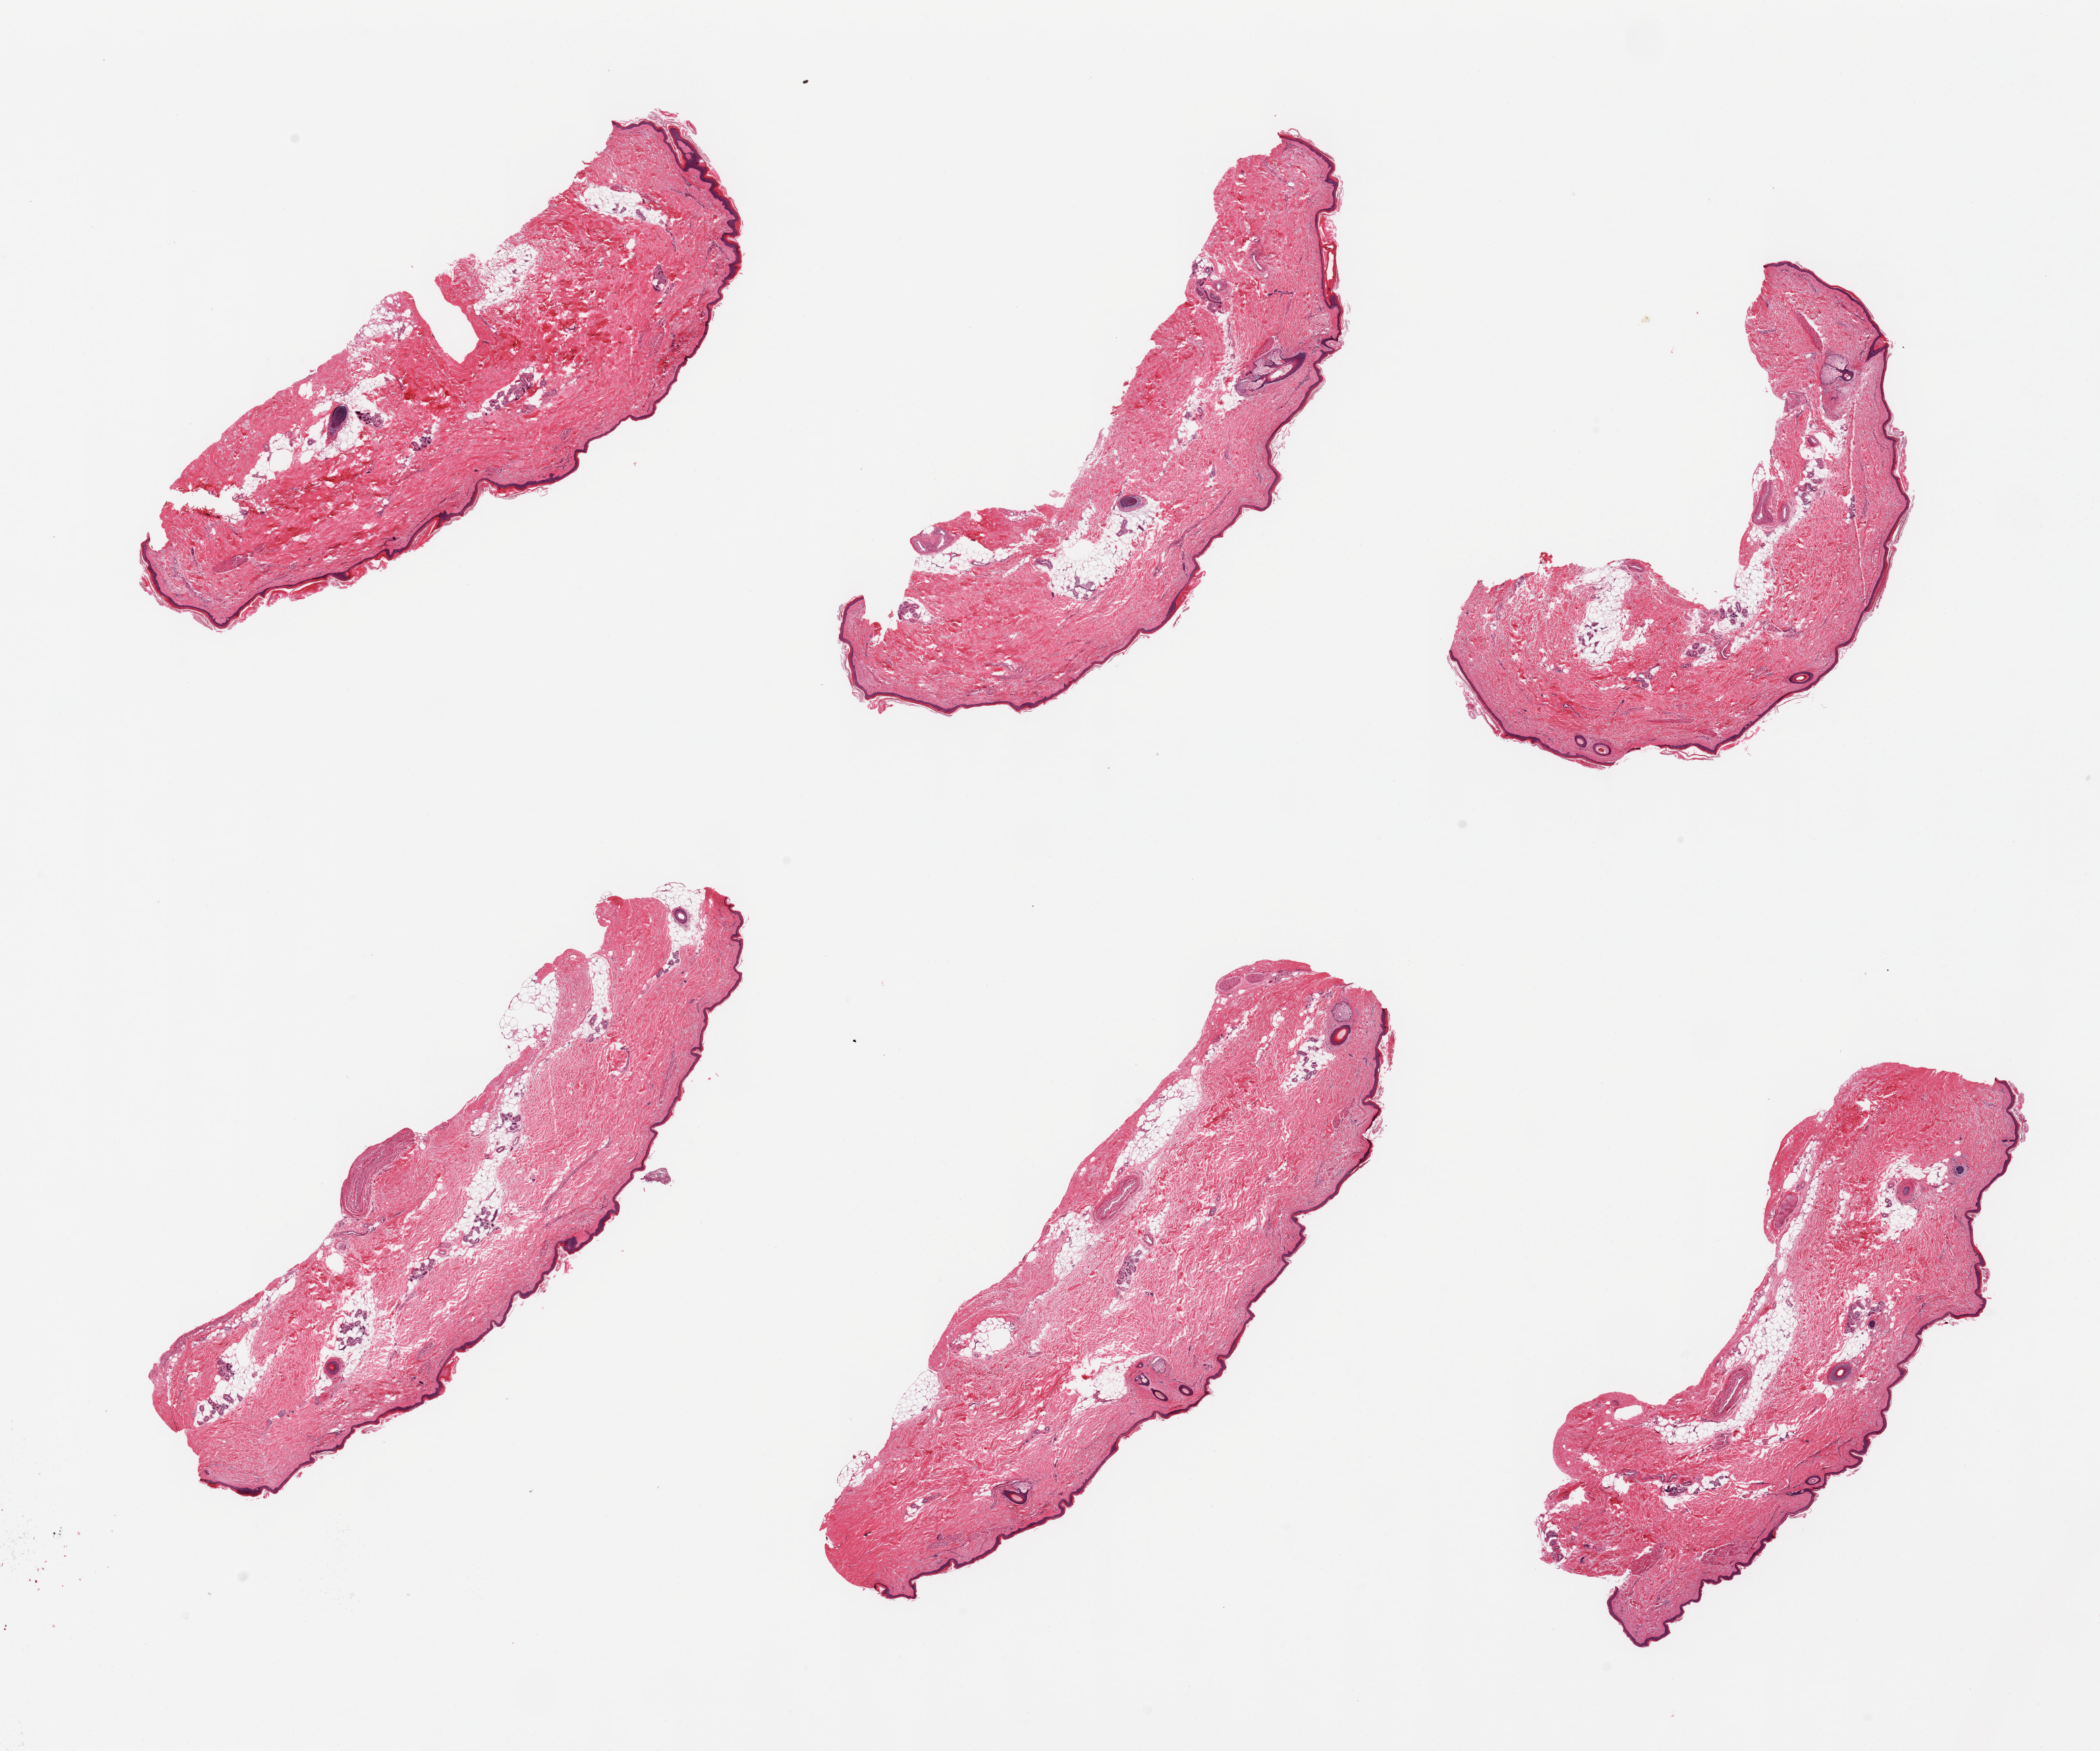
Digitized hematoxylin and eosin (H&E)-stained section, brightfield — low-resolution overview of the scanned area, about 24.6 x 20.5 mm. PAXgene-fixed paraffin-embedded (PFPE) section. Sampled site (target tissue): skin of lower leg. Tissue donor sample. Male donor.
Review note (as recorded): 6 pieces, trace dermal fat; squamous epithelium is ~30 microns.